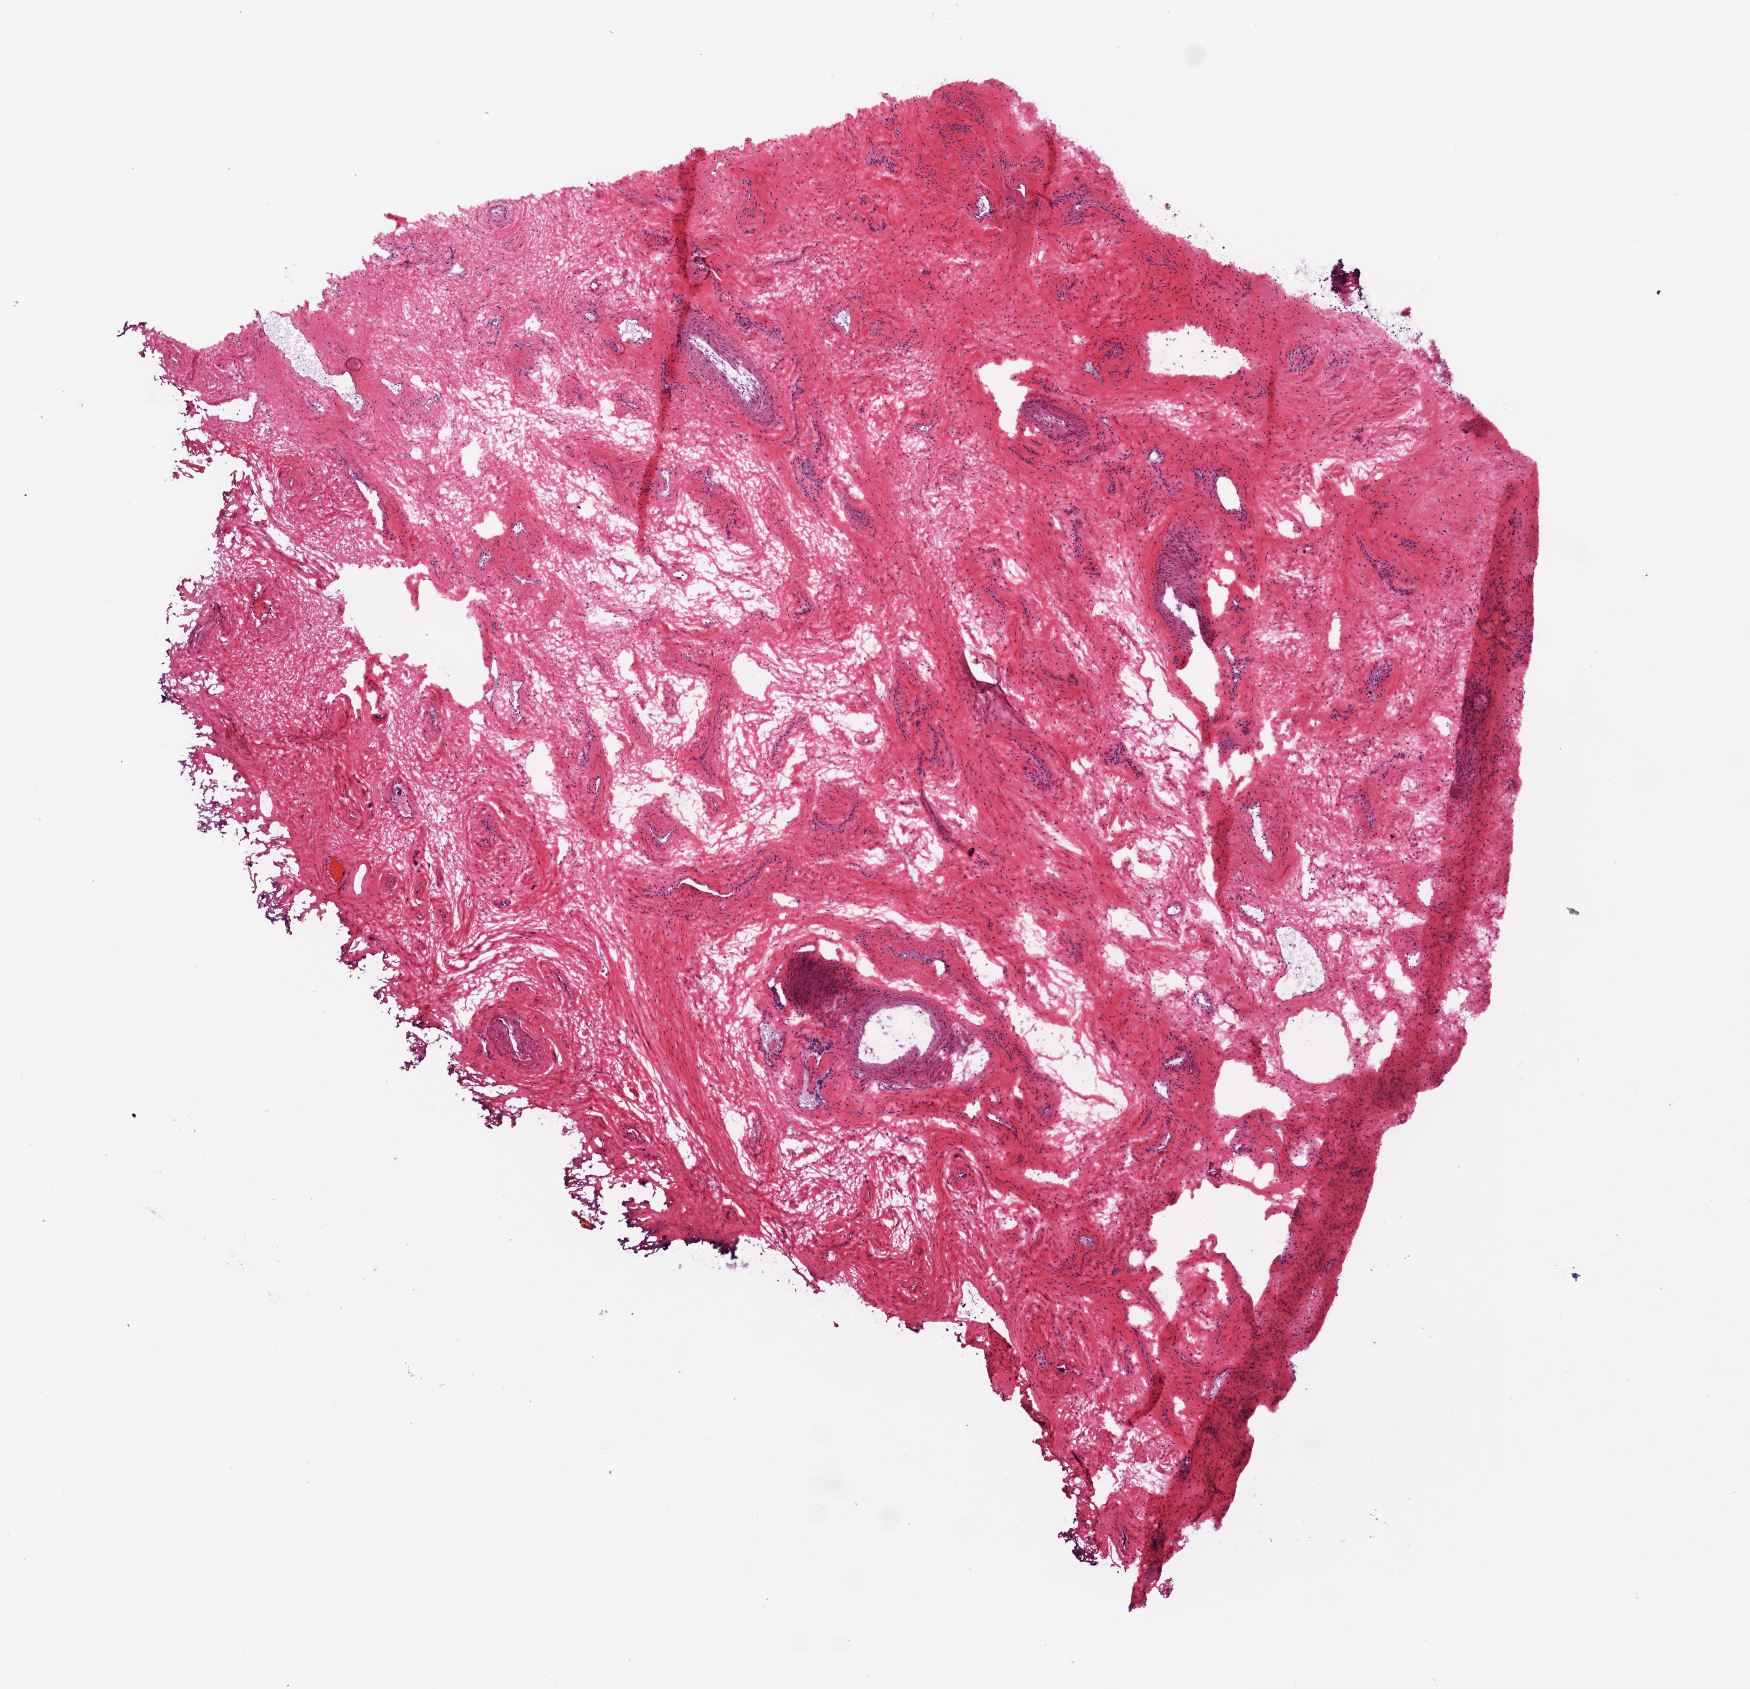
Hematoxylin and eosin (H&E) stained whole-slide image — low-resolution overview of the scanned area, about 7.0 x 6.8 mm (from a 20x scan). Frozen section from the top of the tissue portion. Sample: solid tissue normal (non-tumour tissue), ovary. Female patient; age at initial diagnosis 48 years.
This section: solid tissue normal (non-tumour) sample from the same patient. Patient diagnosis: Serous cystadenocarcinoma, NOS.